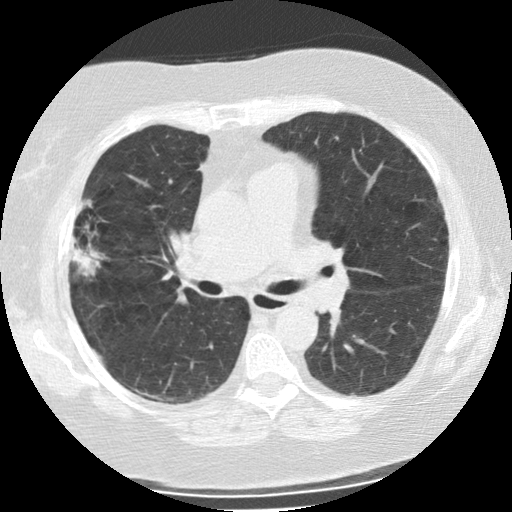
Low-dose screening chest CT, one axial slice; position 135 of 225 along the scan axis; lung window (W 1500 / L -600 HU); 2.5 mm slice thickness; 512 × 512 image matrix, field of view 320 × 320 mm.
Outlined on this slice (expert manual segmentation):
- lesion 1 (tumor, upper lobe of right lung): box from (x=72, y=240) to (x=105, y=276) px